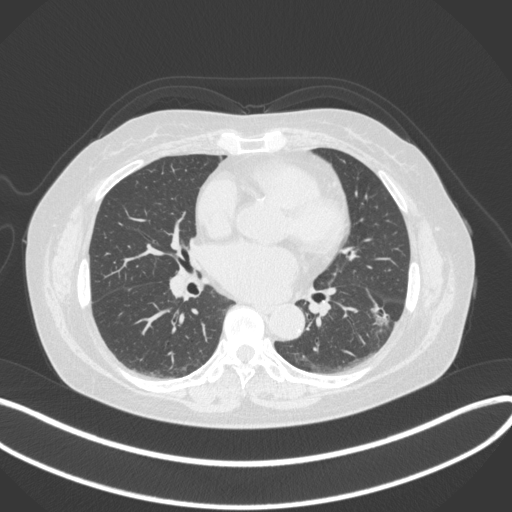
Chest CT, one axial slice. Slice 172 of 373 in the series (ordered by position). Reconstruction kernel B31f. Lung window (W 1500 / L -600 HU). 512 × 512 image matrix. Female patient, age 67 years. From the clinical record (not read from this slice): clinical TNM (as recorded): T1c N0 M0.
Structures marked on this image (bounding box drawn by a radiologist):
- lung tumour (recorded histology: adenocarcinoma): bounding box (x1, y1, x2, y2) in pixels: (364, 293, 398, 332)